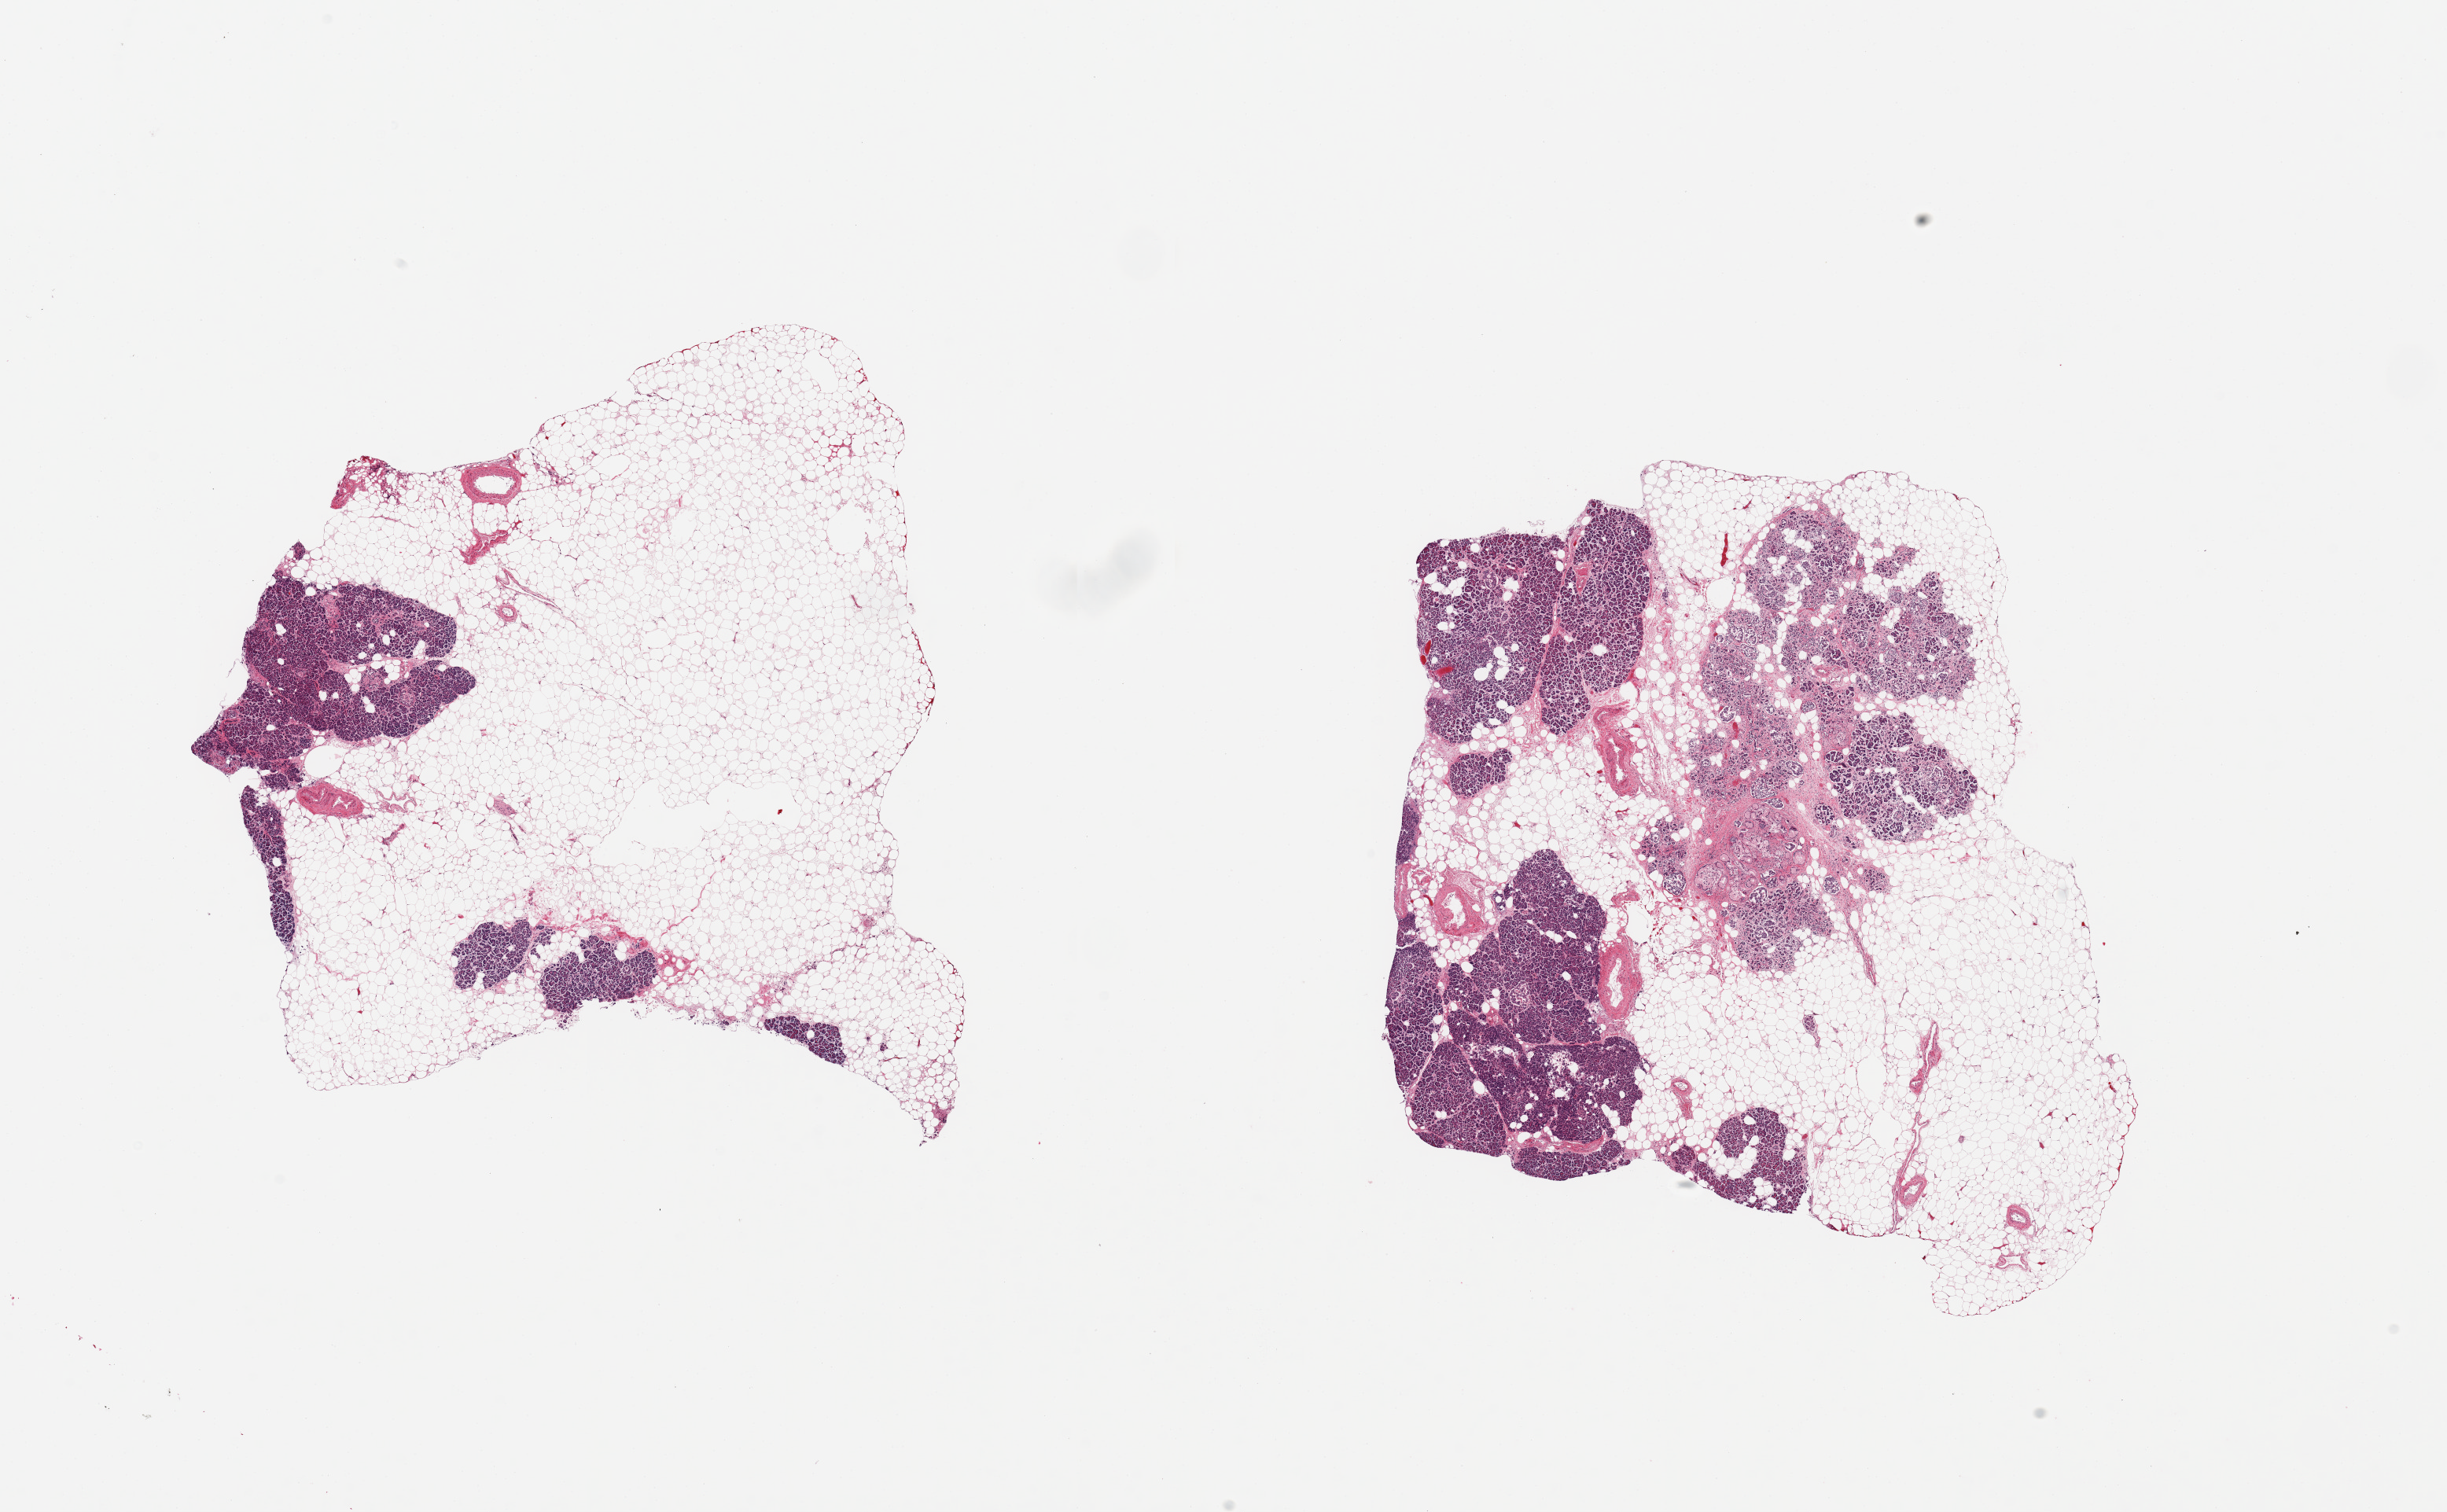
Hematoxylin and eosin (H&E) whole-slide image — a low-resolution overview of the entire scanned area, about 24.6 x 15.2 mm (slide scanned at 20x). Donor sex: female.
Specimen: PAXgene-fixed, paraffin-embedded tissue; section of pancreas (target tissue); tissue donor sample.